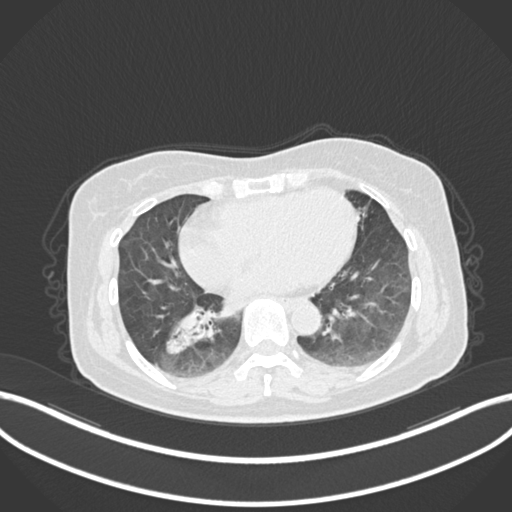
Chest CT, one axial slice. Position 53 of 222 along the scan axis. Reconstruction kernel B30f. Lung window (W 1500 / L -600 HU). 1 mm slice thickness. 512 × 512 image matrix, field of view 400 × 400 mm. Patient: female, 67 years. Case-level facts recorded for this patient, not image findings: clinical TNM (as recorded): T1c N1 M0.
Outlined on this slice (rectangle marked by the reading radiologist):
- lung tumour (recorded histology: adenocarcinoma): bounding box [x1, y1, x2, y2] px = [169, 304, 221, 358]